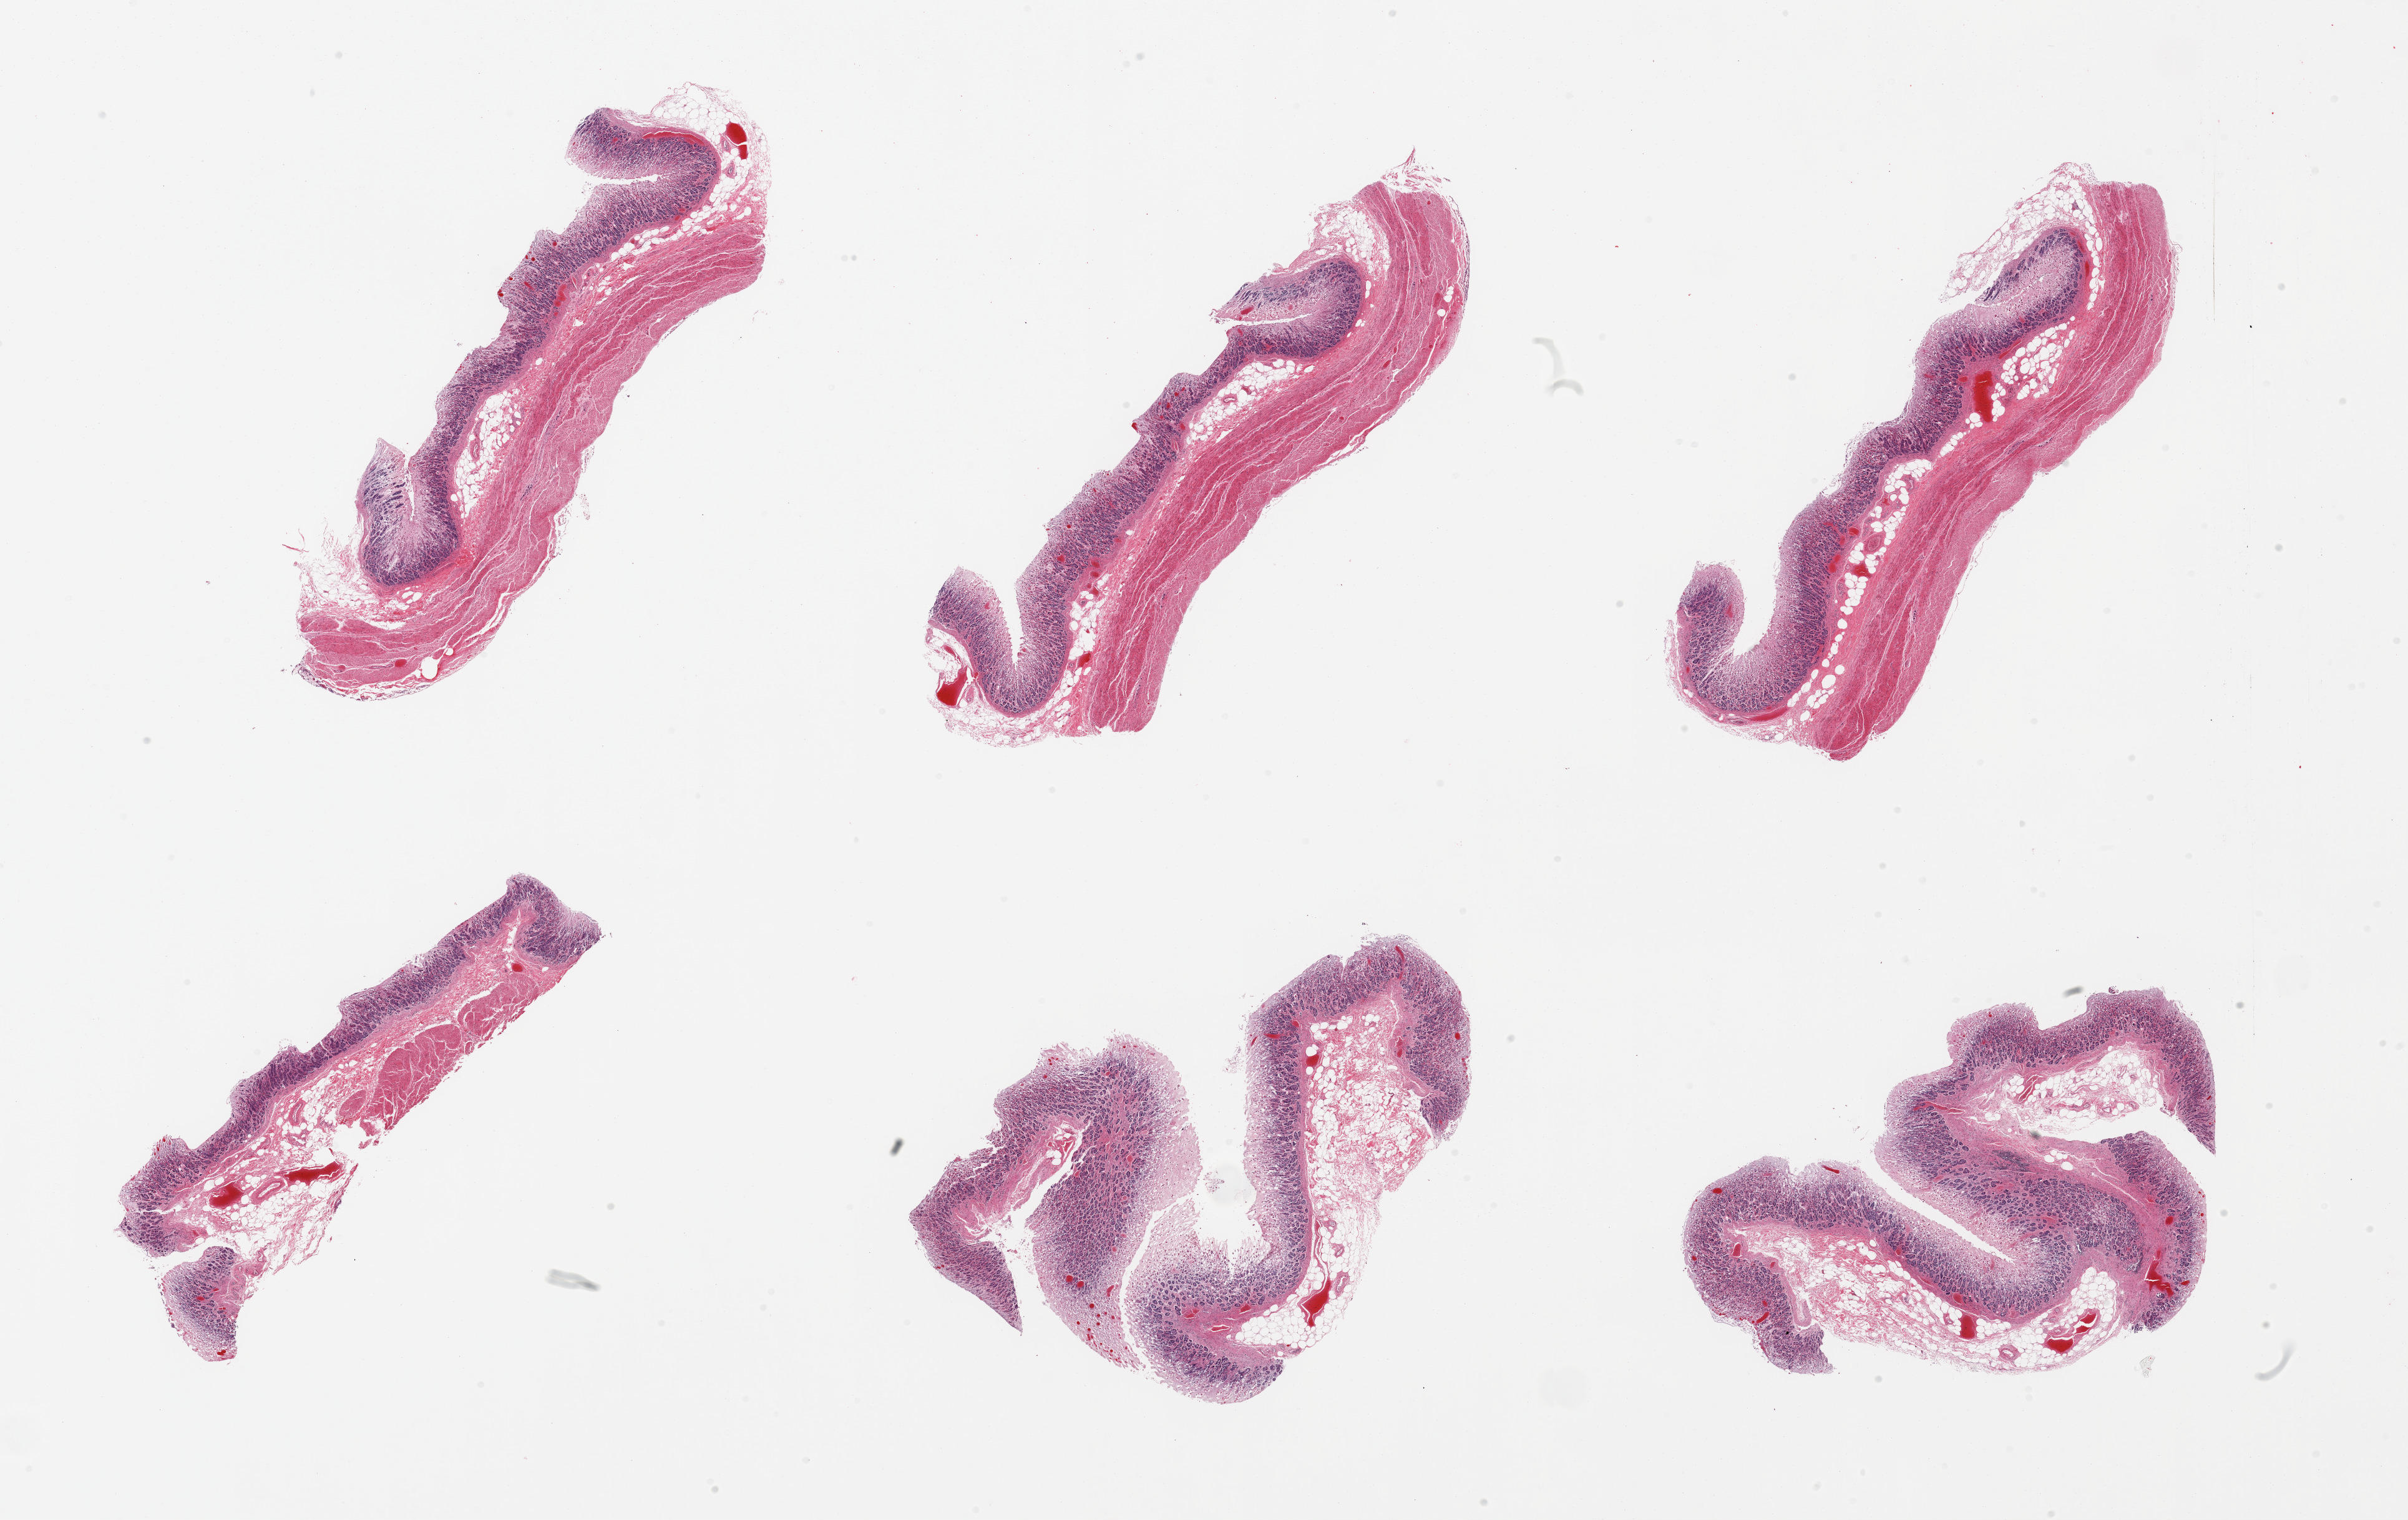
Whole-slide image, haematoxylin and eosin stain, shown as a low-resolution overview of the whole scanned area (about 30.5 x 19.3 mm, from a 20x scan). PAXgene-fixed paraffin-embedded (PFPE) section. Target tissue: stomach. Donor tissue sample. Male donor.
- review note (as recorded): 6 pieces; 4 include mucosa and muscularis, 2 are mucosa/submucosa only; focal grade 3 mucosal autolysis; congestion